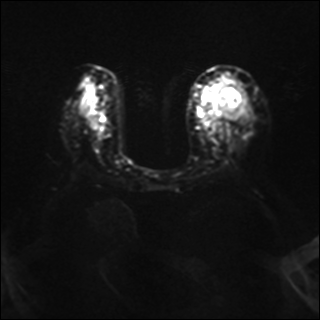
Breast MRI, one axial slice; position 18 of 37 along the scan axis; diffusion-weighted series; image 2 of 4 stored at this slice position (different b-values; order by instance number); 1.5 T; 320 × 320 image matrix, field of view 320 × 320 mm. Female patient.
Annotated regions visible in this slice (expert manual segmentation):
- tumour on diffusion-weighted imaging: bounding box [x1, y1, x2, y2] px = [217, 85, 239, 113]